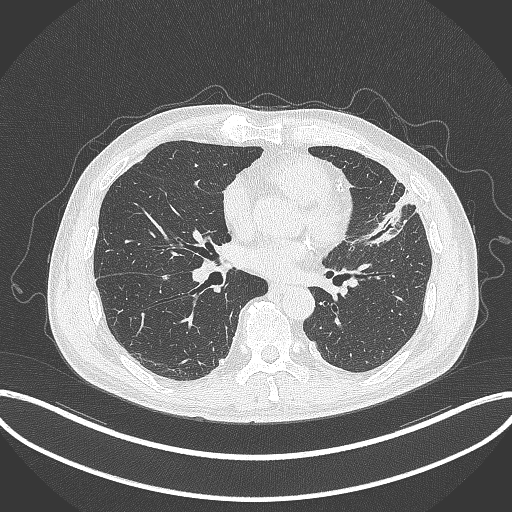
Chest CT, one axial slice; slice 151 of 382 in the series (ordered by position); 120 kVp; lung window (W 1500 / L -600 HU); 1 mm slice thickness; 512 × 512 image matrix. Patient: male, 64 years. Case-level facts recorded for this patient, not image findings: clinical TNM (as recorded): T4 N1 M0; histopathological grade: G3.
Outlined on this slice (bounding box drawn by a radiologist):
- lung tumour (recorded histology: adenocarcinoma): bounding box [x1, y1, x2, y2] px = [358, 182, 423, 250]